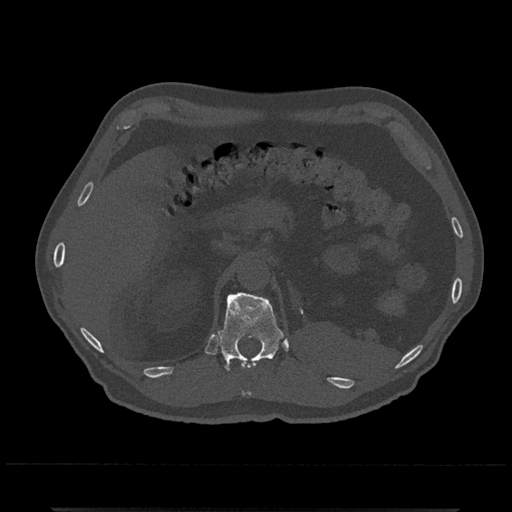
CT including the spine, one axial slice. Position 442 of 797 along the scan axis. 120 kVp. Bone window (W 1800 / L 400 HU). 512 × 512 image matrix, field of view 393 × 393 mm. Male patient, age 67 years. Case-level facts recorded for this patient, not image findings: primary cancer: prostate.
Outlined on this slice (semi-automatically segmented with operator editing):
- T11 vertebra: bounding box <243,361,256,396> (left, top, right, bottom; pixels)
- T12 vertebra: <217,292,284,372>